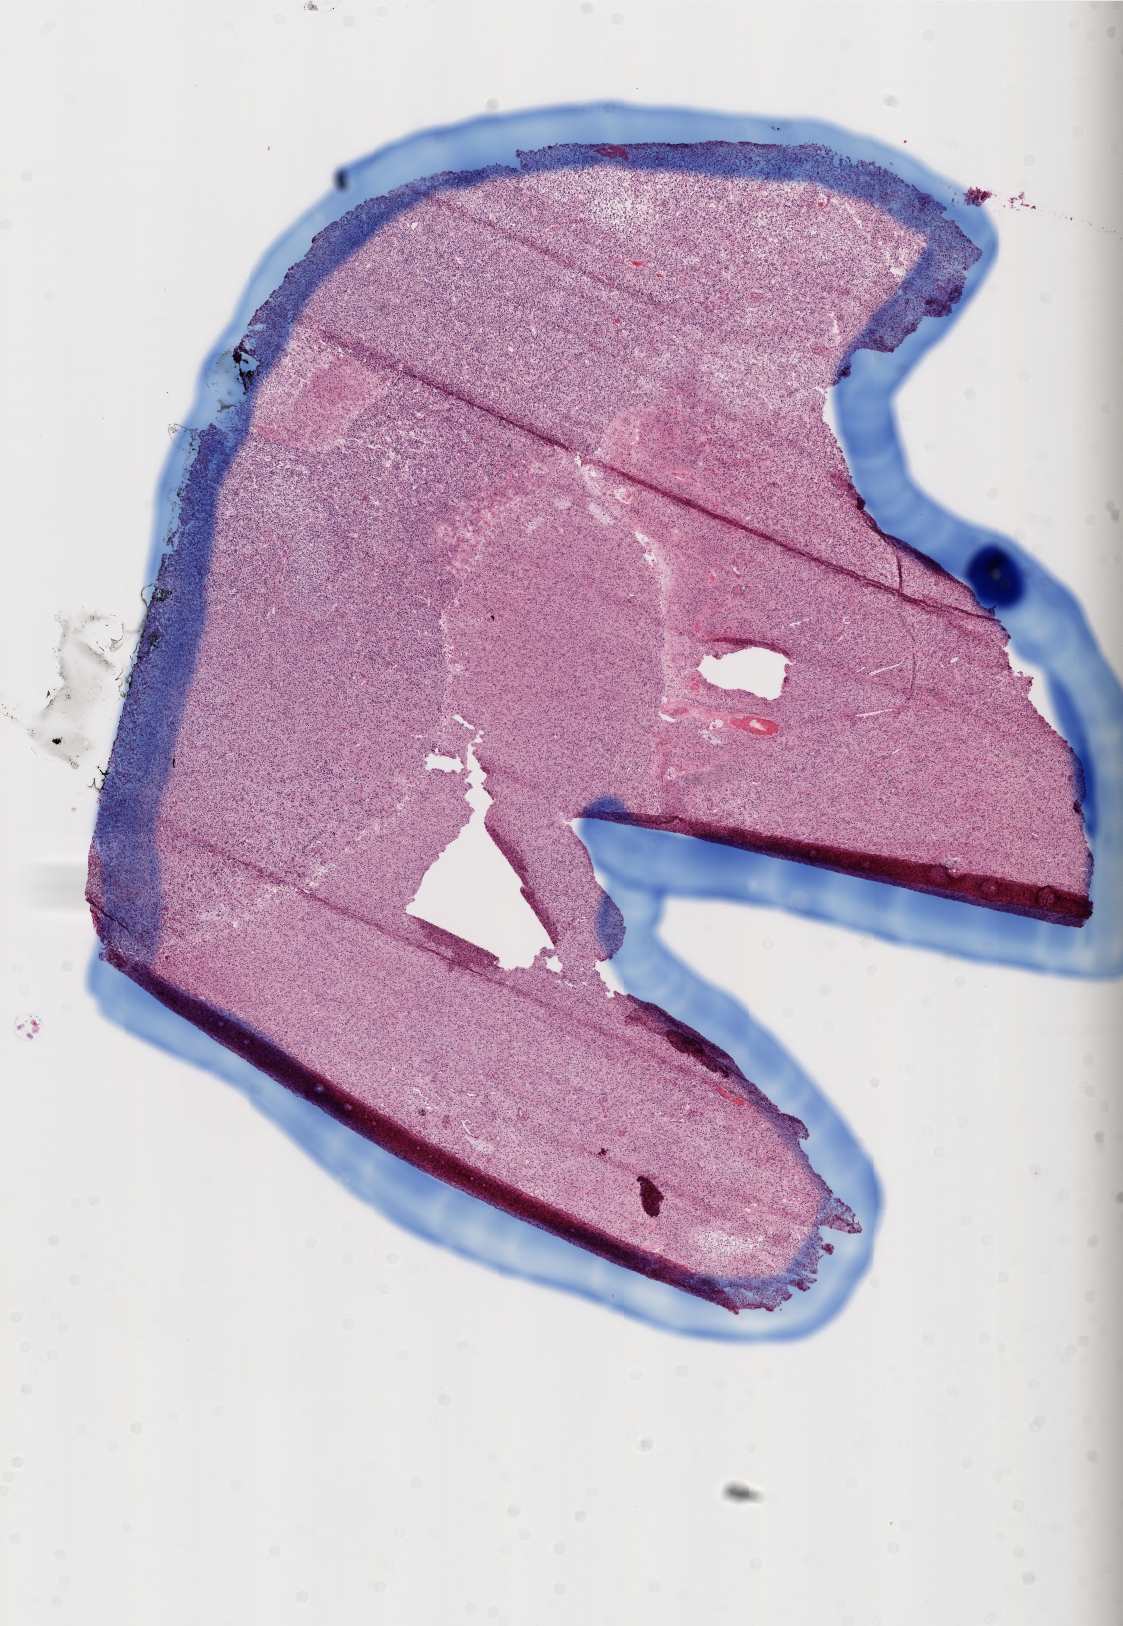
Digitized H&E tissue section (whole slide) — low-resolution overview of the scanned area, about 9.0 x 13.0 mm, frozen section from the top of the tissue portion, brain, primary tumour sample. Male patient; age at initial diagnosis 54 years.
Histologic diagnosis: Glioblastoma.